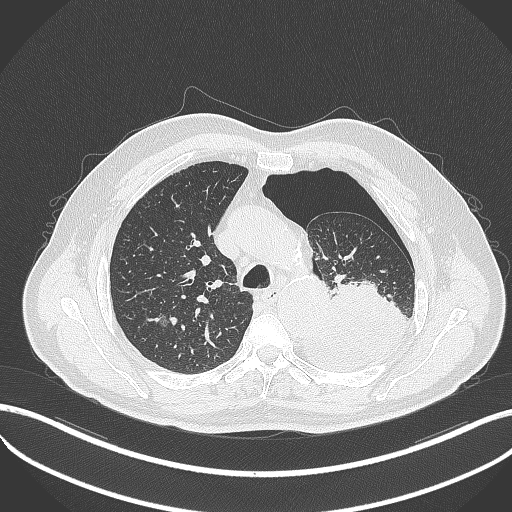
Chest CT, one axial slice. Slice 367 of 464 in the series (ordered by position). 120 kVp. Lung window (W 1500 / L -600 HU). 1 mm slice thickness. 512 × 512 image matrix, field of view 400 × 400 mm. Patient: male, 76 years. Case-level facts recorded for this patient, not image findings: clinical TNM (as recorded): T3 N0 M1b.
Outlined on this slice (bounding box drawn by a radiologist):
- lung tumour (recorded histology: adenocarcinoma): bounding box [x1, y1, x2, y2] px = [303, 282, 412, 372]